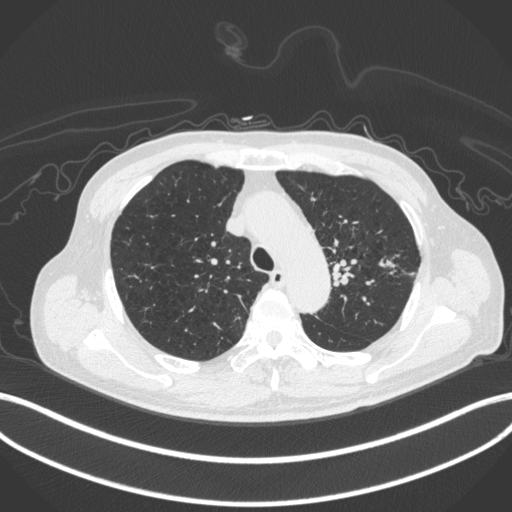
Chest CT, one axial slice; position 328 of 420 along the scan axis; reconstruction kernel B31f; 120 kVp; lung window (W 1500 / L -600 HU); 1 mm slice thickness; 512 × 512 image matrix, field of view 400 × 400 mm. Male patient, age 77 years. From the clinical record (not read from this slice): clinical TNM (as recorded): T3 N1 M0.
Outlined on this slice (rectangle marked by the reading radiologist):
- lung tumour (recorded histology: adenocarcinoma): bounding box [x1, y1, x2, y2] px = [376, 257, 398, 271]